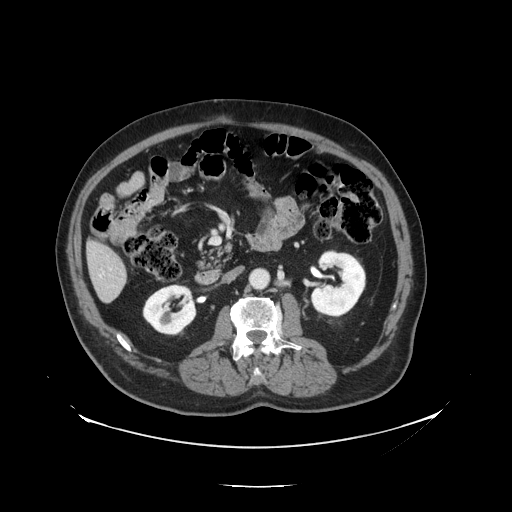
Contrast-enhanced abdominal CT, one axial slice. Reconstruction kernel STANDARD. Intravenous contrast given. Soft-tissue window (W 400 / L 40 HU). 2.5 mm slice thickness. 512 × 512 image matrix, field of view 497 × 497 mm. Male patient, age 77 years. Case-level facts recorded for this patient, not image findings: diagnosis: colorectal cancer liver metastases, imaged before liver resection; multiple liver metastases: no; largest metastasis: 1.5 cm.
Structures marked on this image (expert manual segmentation):
- liver: bounding box [x1, y1, x2, y2] px = [89, 243, 127, 303]
- planned liver remnant (the part of the liver to remain after resection): [89, 242, 125, 277]